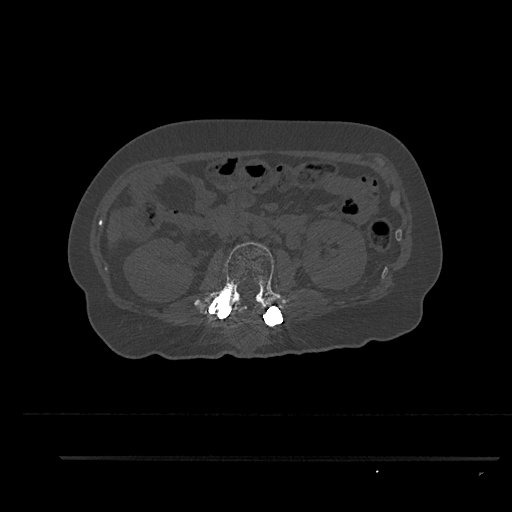
CT including the spine, one axial slice; position 161 of 797 along the scan axis; reconstruction kernel Br40s/3; 120 kVp; bone window (W 1800 / L 400 HU); 0.5 mm slice thickness; 512 × 512 image matrix. Patient: female, 44 years. From the clinical record (not read from this slice): primary cancer: renal.
Annotated regions visible in this slice (semi-automatically segmented with operator editing):
- L2 vertebra: bounding box [x1, y1, x2, y2] px = [193, 242, 285, 319]